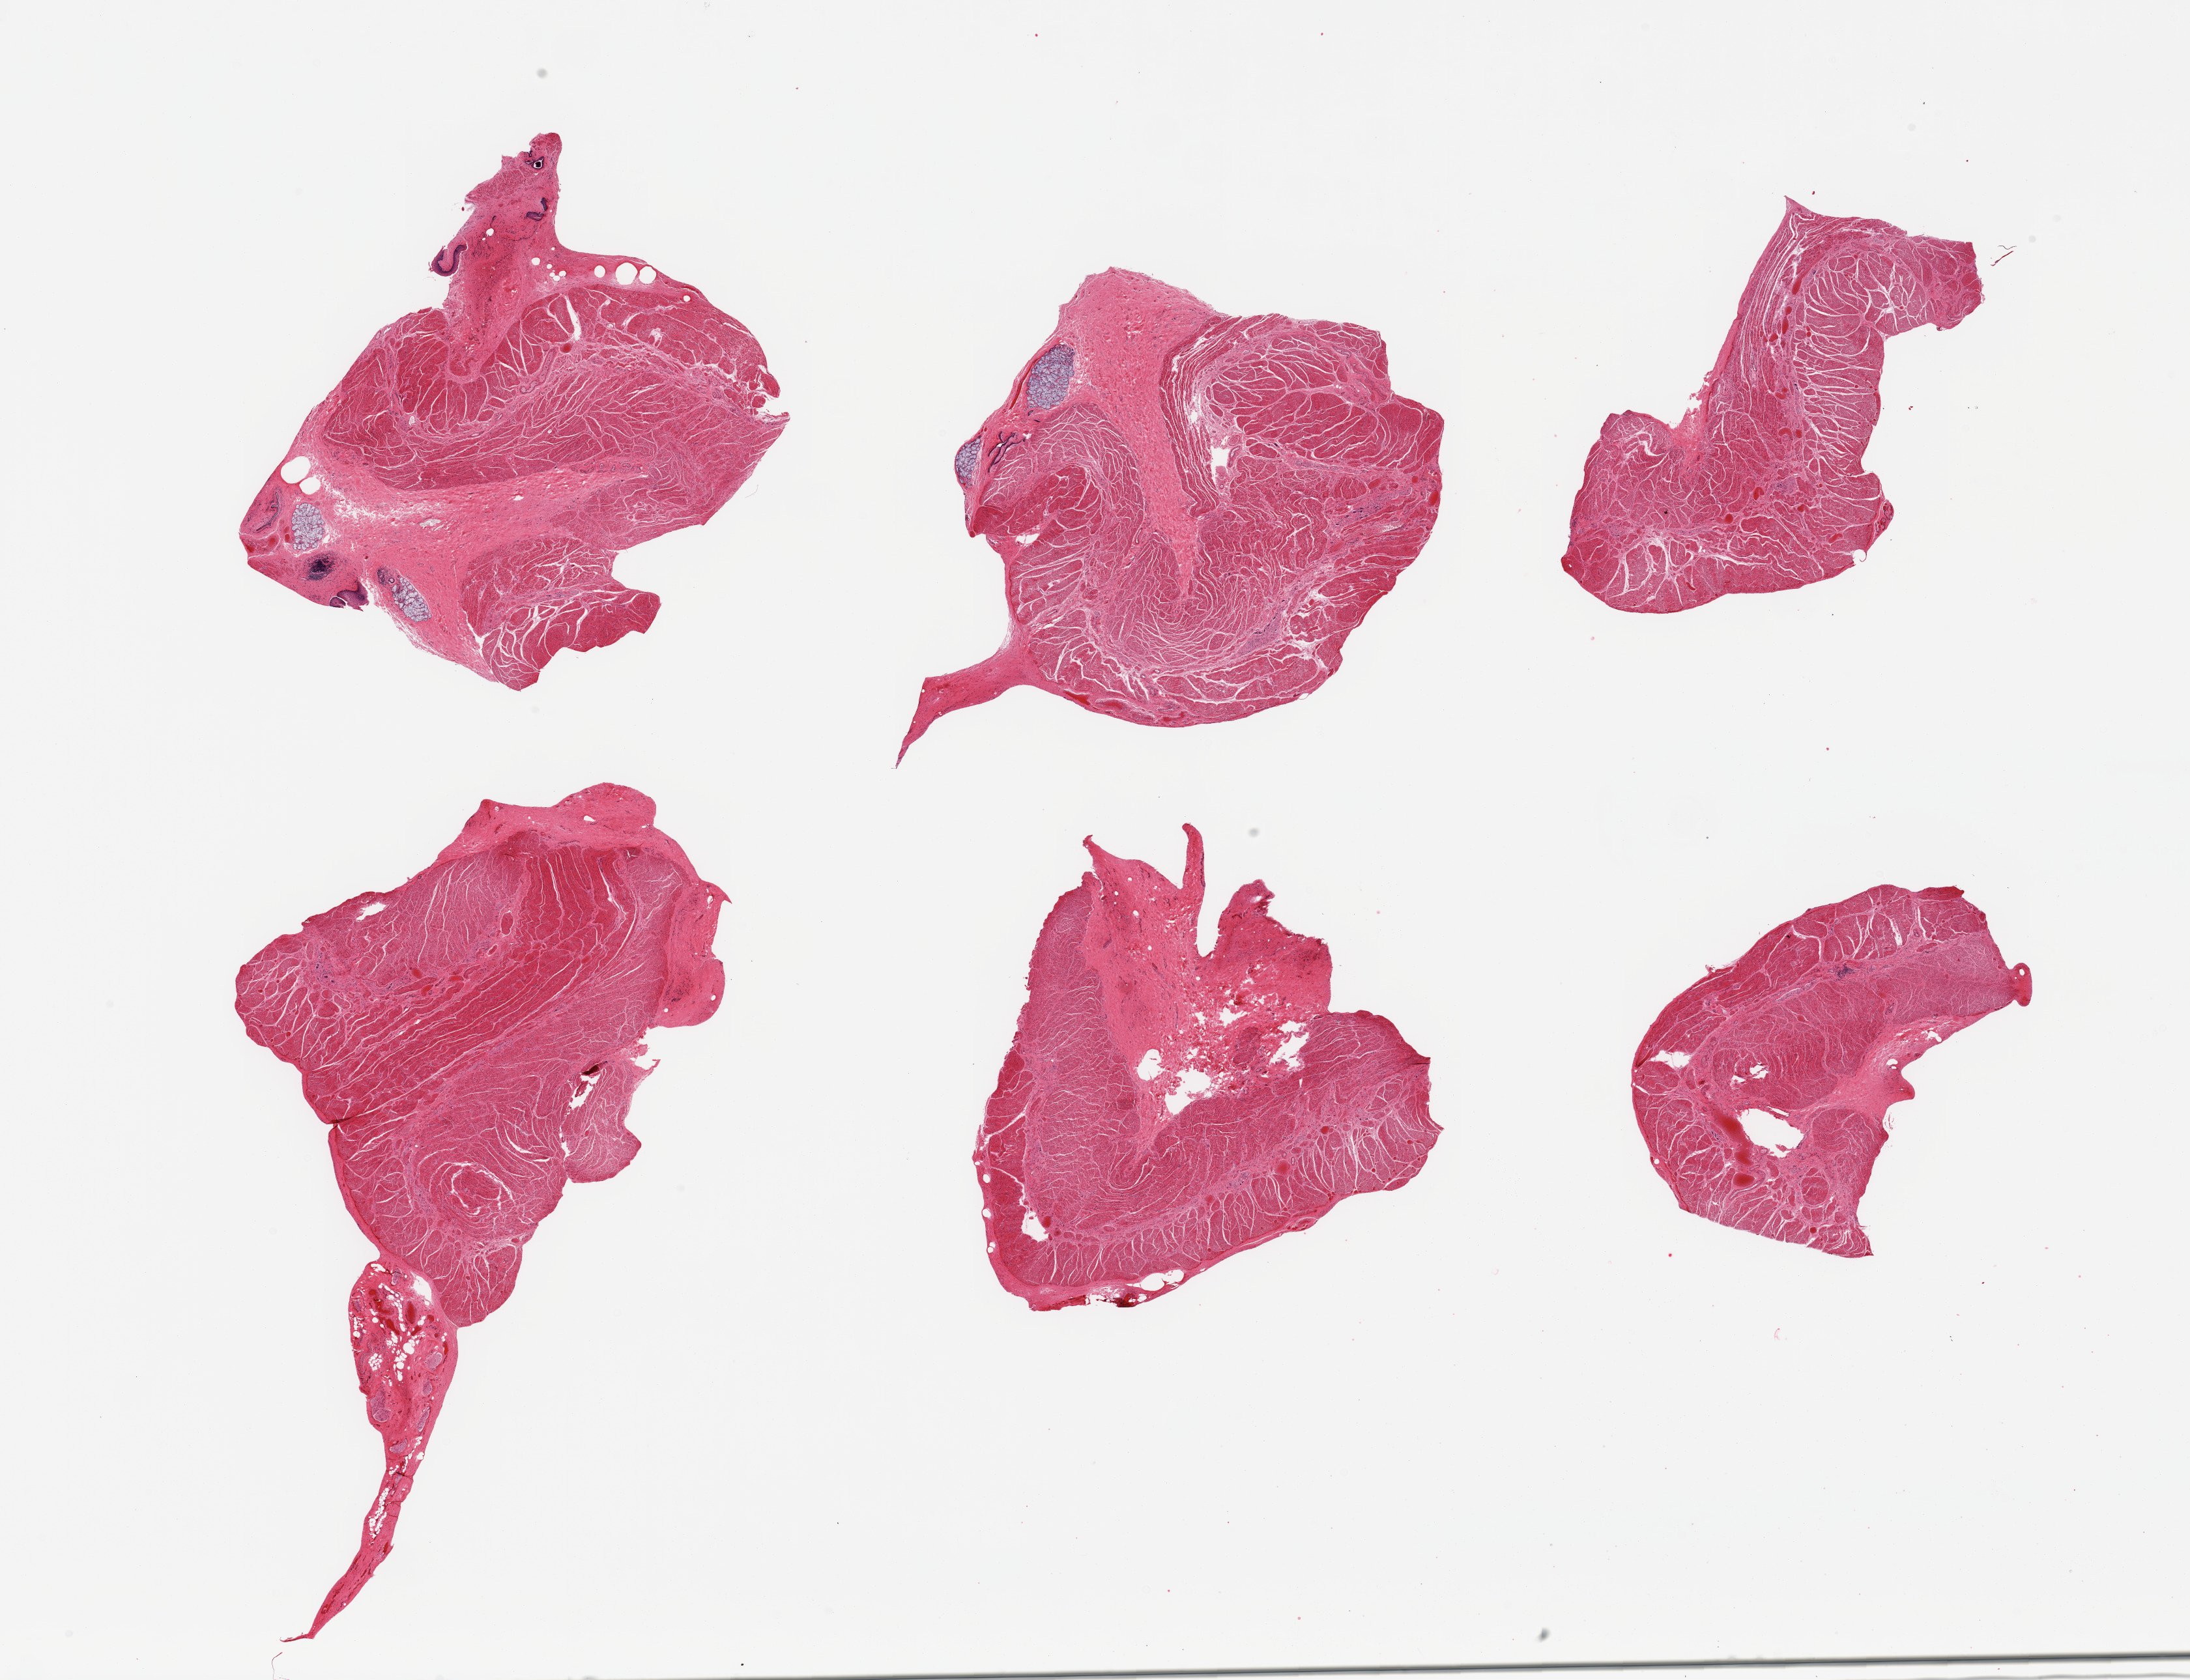
H&E whole-slide image, whole scanned area (about 26.6 x 20.4 mm, acquisition: 20x scan) shown as a low-resolution overview. PAXgene-fixed paraffin-embedded (PFPE) section. Section of gastroesophageal junction (target tissue). Donor tissue sample.
Review note (as recorded): 6 pieces; mostly target muscularis with small strips of residual squamous mucosa and submucosal glands.